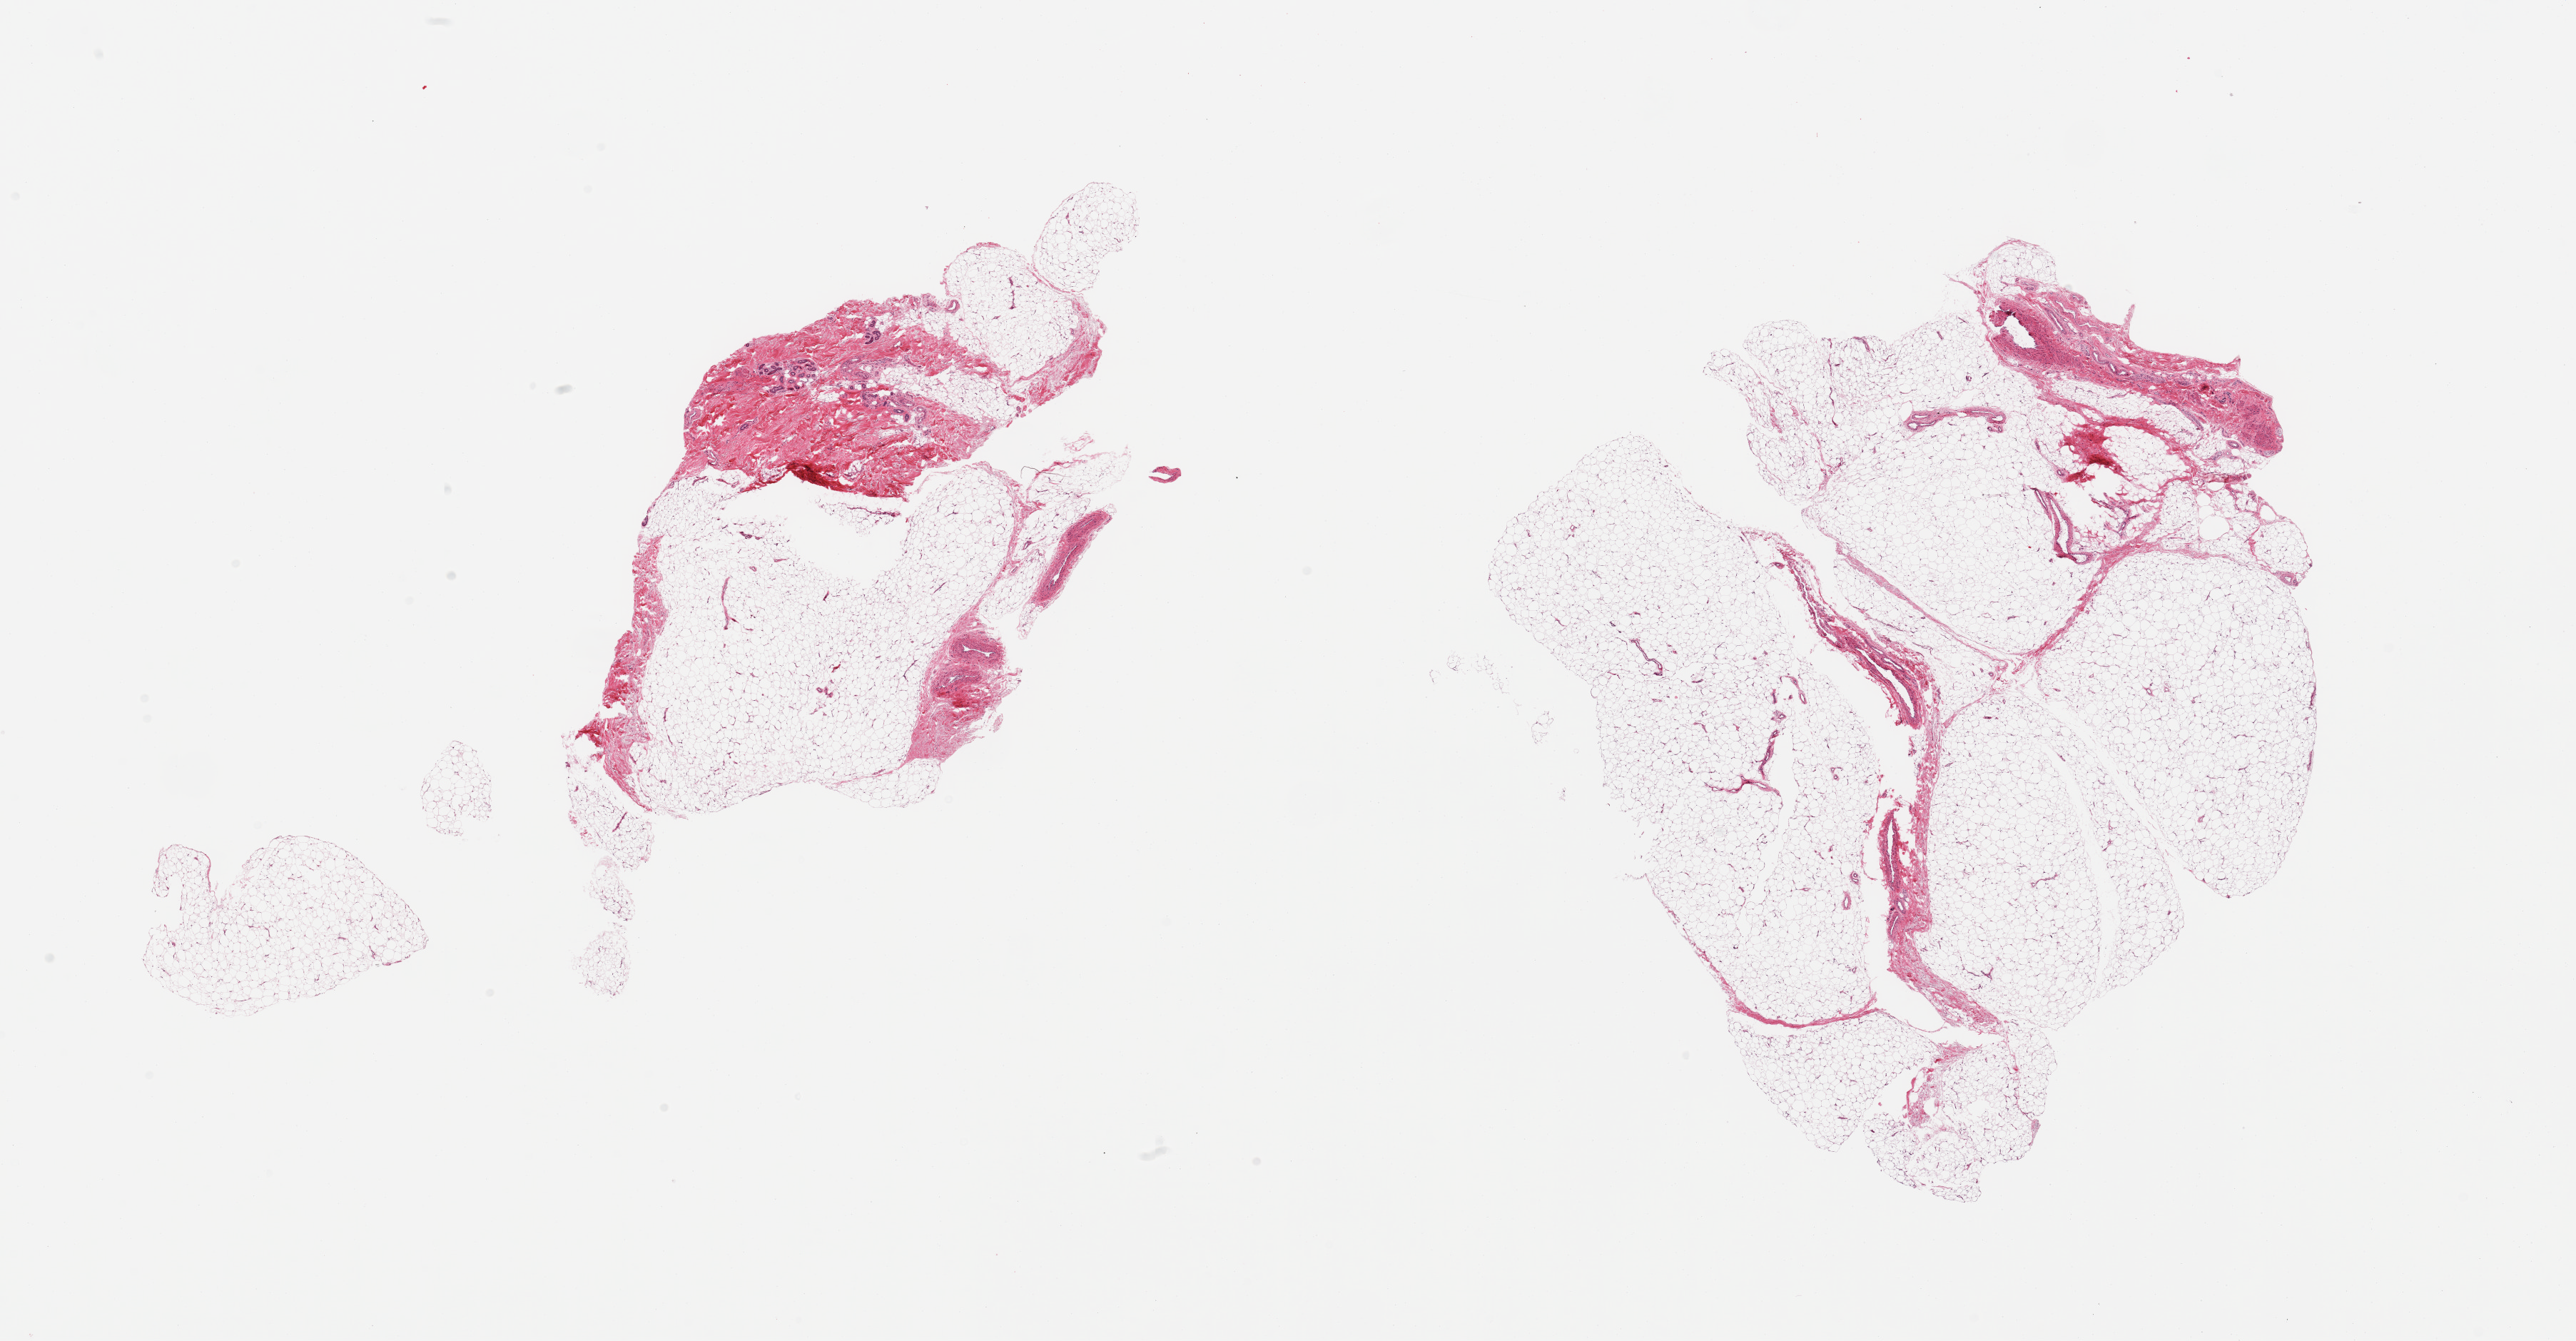
Digitized haematoxylin and eosin-stained section, brightfield, shown as a low-resolution overview of the whole scanned area (about 28.5 x 14.9 mm, from a 20x scan). PAXgene-fixed, paraffin-embedded tissue. Target tissue: adipose tissue. Donor tissue sample. Donor: male.
- reviewer comment on this tissue sample: 2 pieces; 30% and 15% facia/vessels/glands